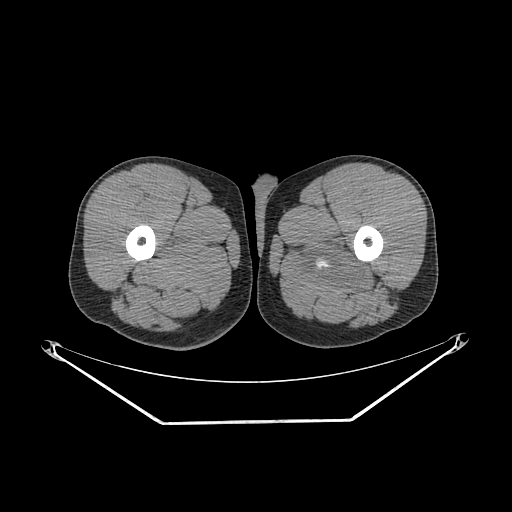
CT of an extremity soft-tissue mass (from a PET/CT study), one axial slice. Soft-tissue window (W 400 / L 40 HU). 3.75 mm slice thickness. 512 × 512 image matrix. Male patient. From the clinical record (not read from this slice): histological type: extraskeletal osteosarcoma; grade: high; site of the primary tumour: left adductur.
Structures marked on this image (expert contour drawn on MRI and transferred to this co-registered scan by the dataset authors):
- gross tumour volume (mass): bounding box <288,230,378,296> (left, top, right, bottom; pixels)